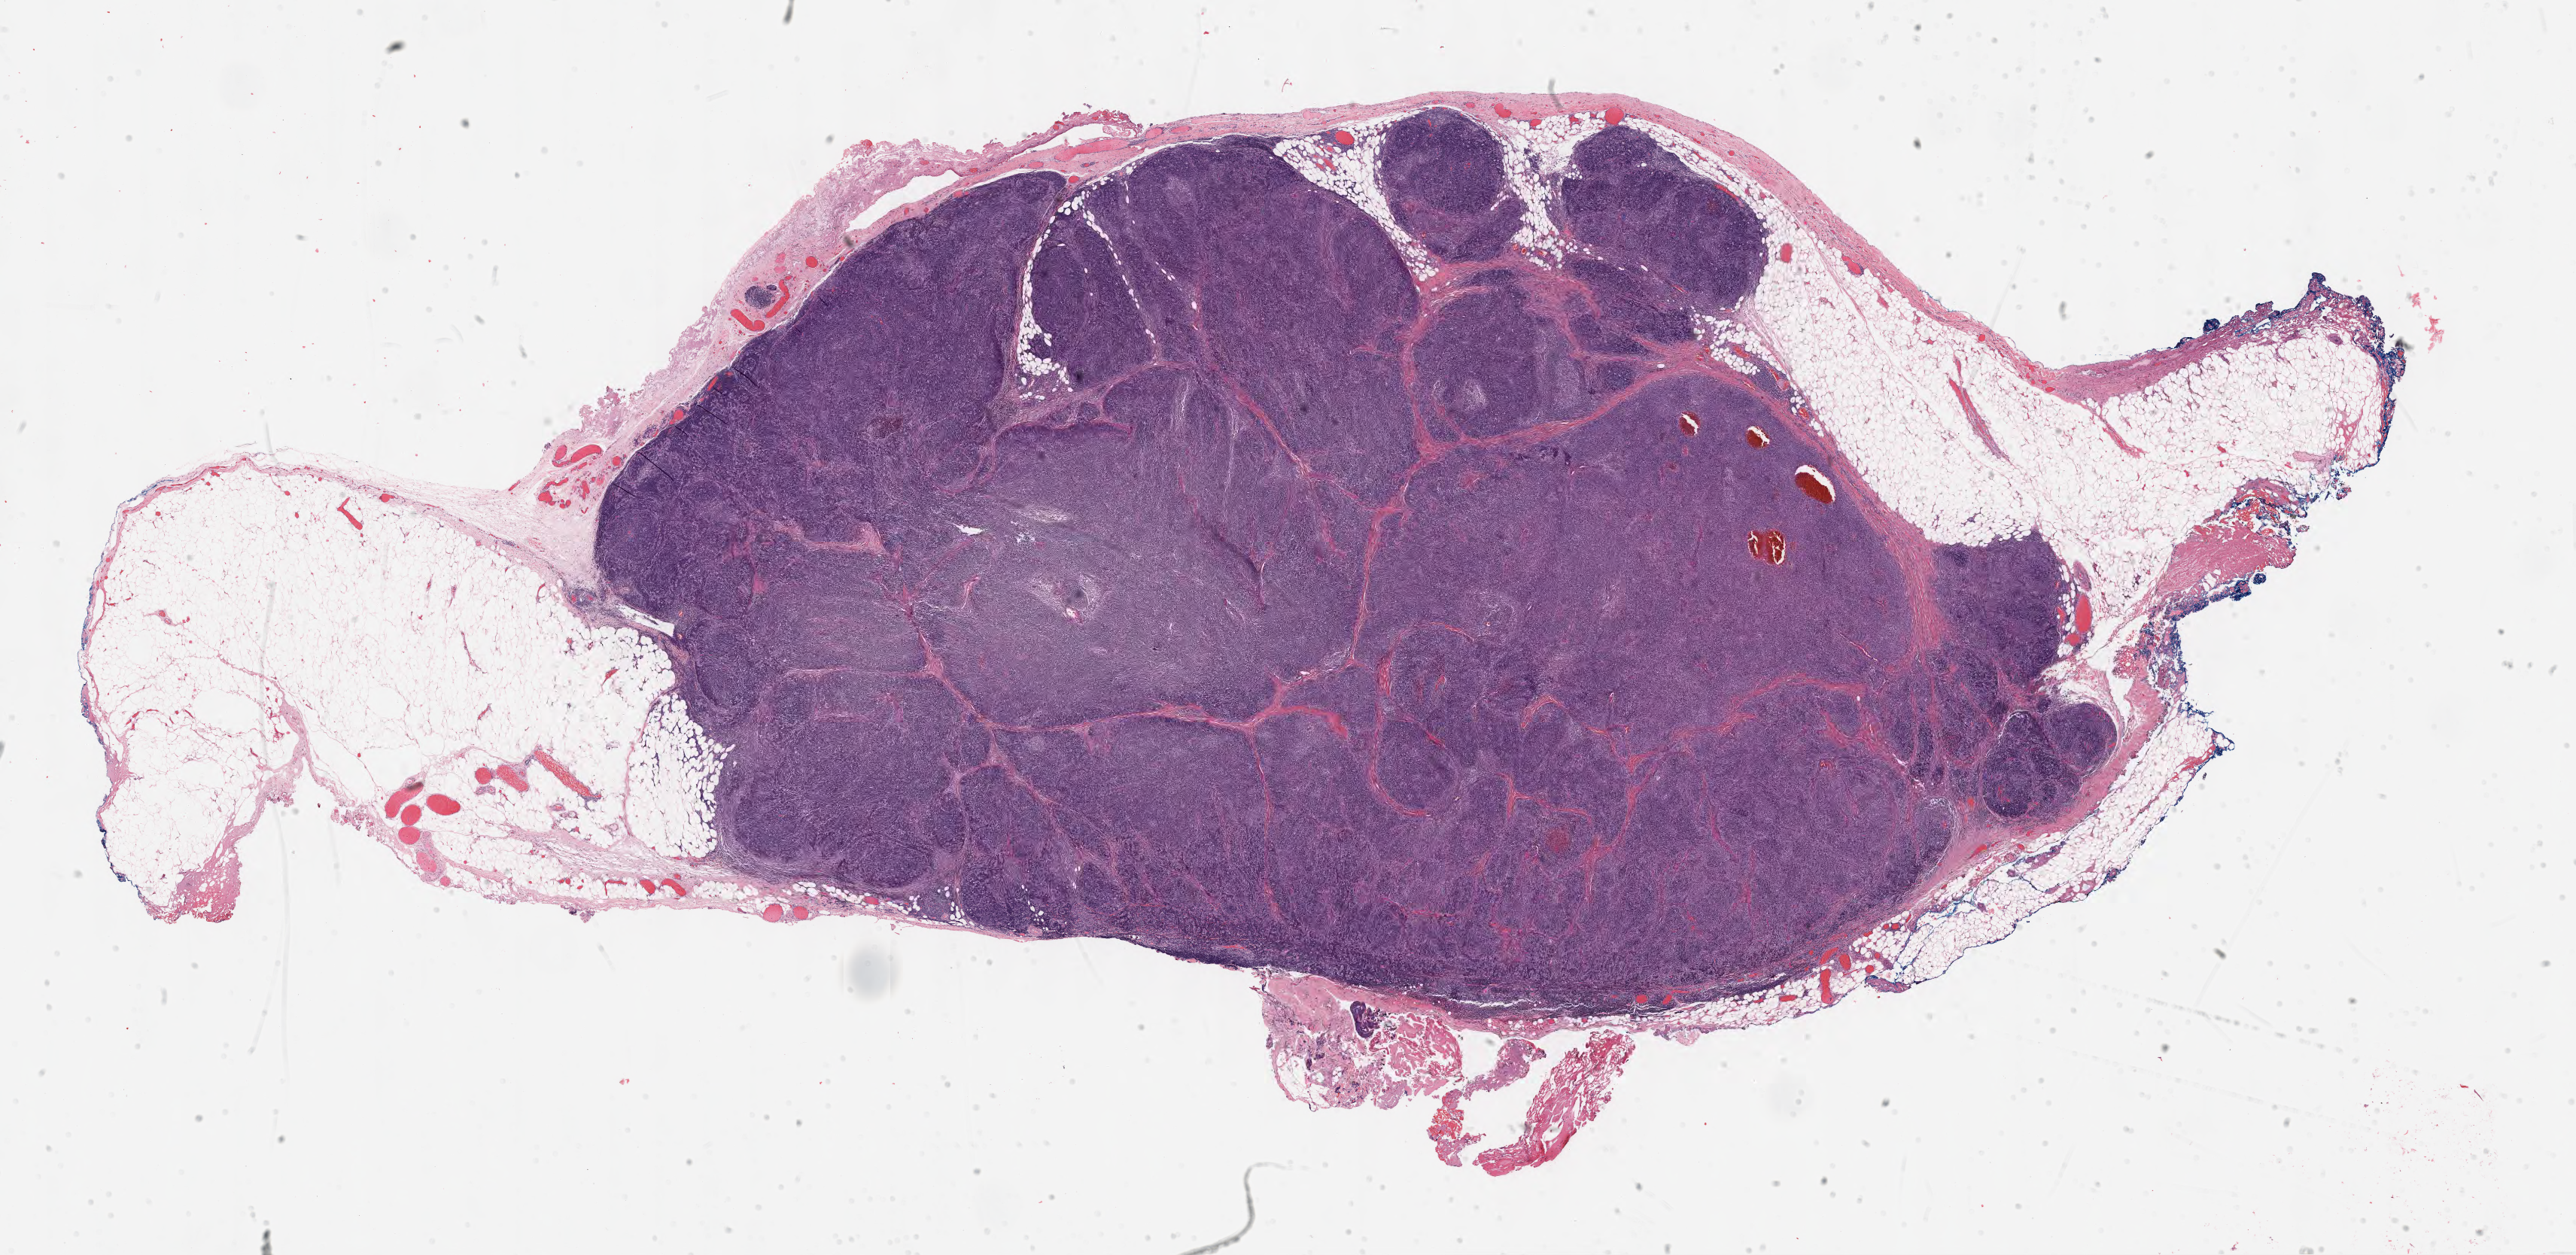
Digitized H&E-stained tissue section (whole slide), whole scanned area (about 27.7 x 13.5 mm, slide scanned at 40x) shown as a low-resolution overview. Formalin-fixed paraffin-embedded (FFPE) diagnostic section. Primary tumour sample from the thymus. Patient: male, age at initial diagnosis 45 years.
Histologic diagnosis: Thymoma, type B1, malignant.